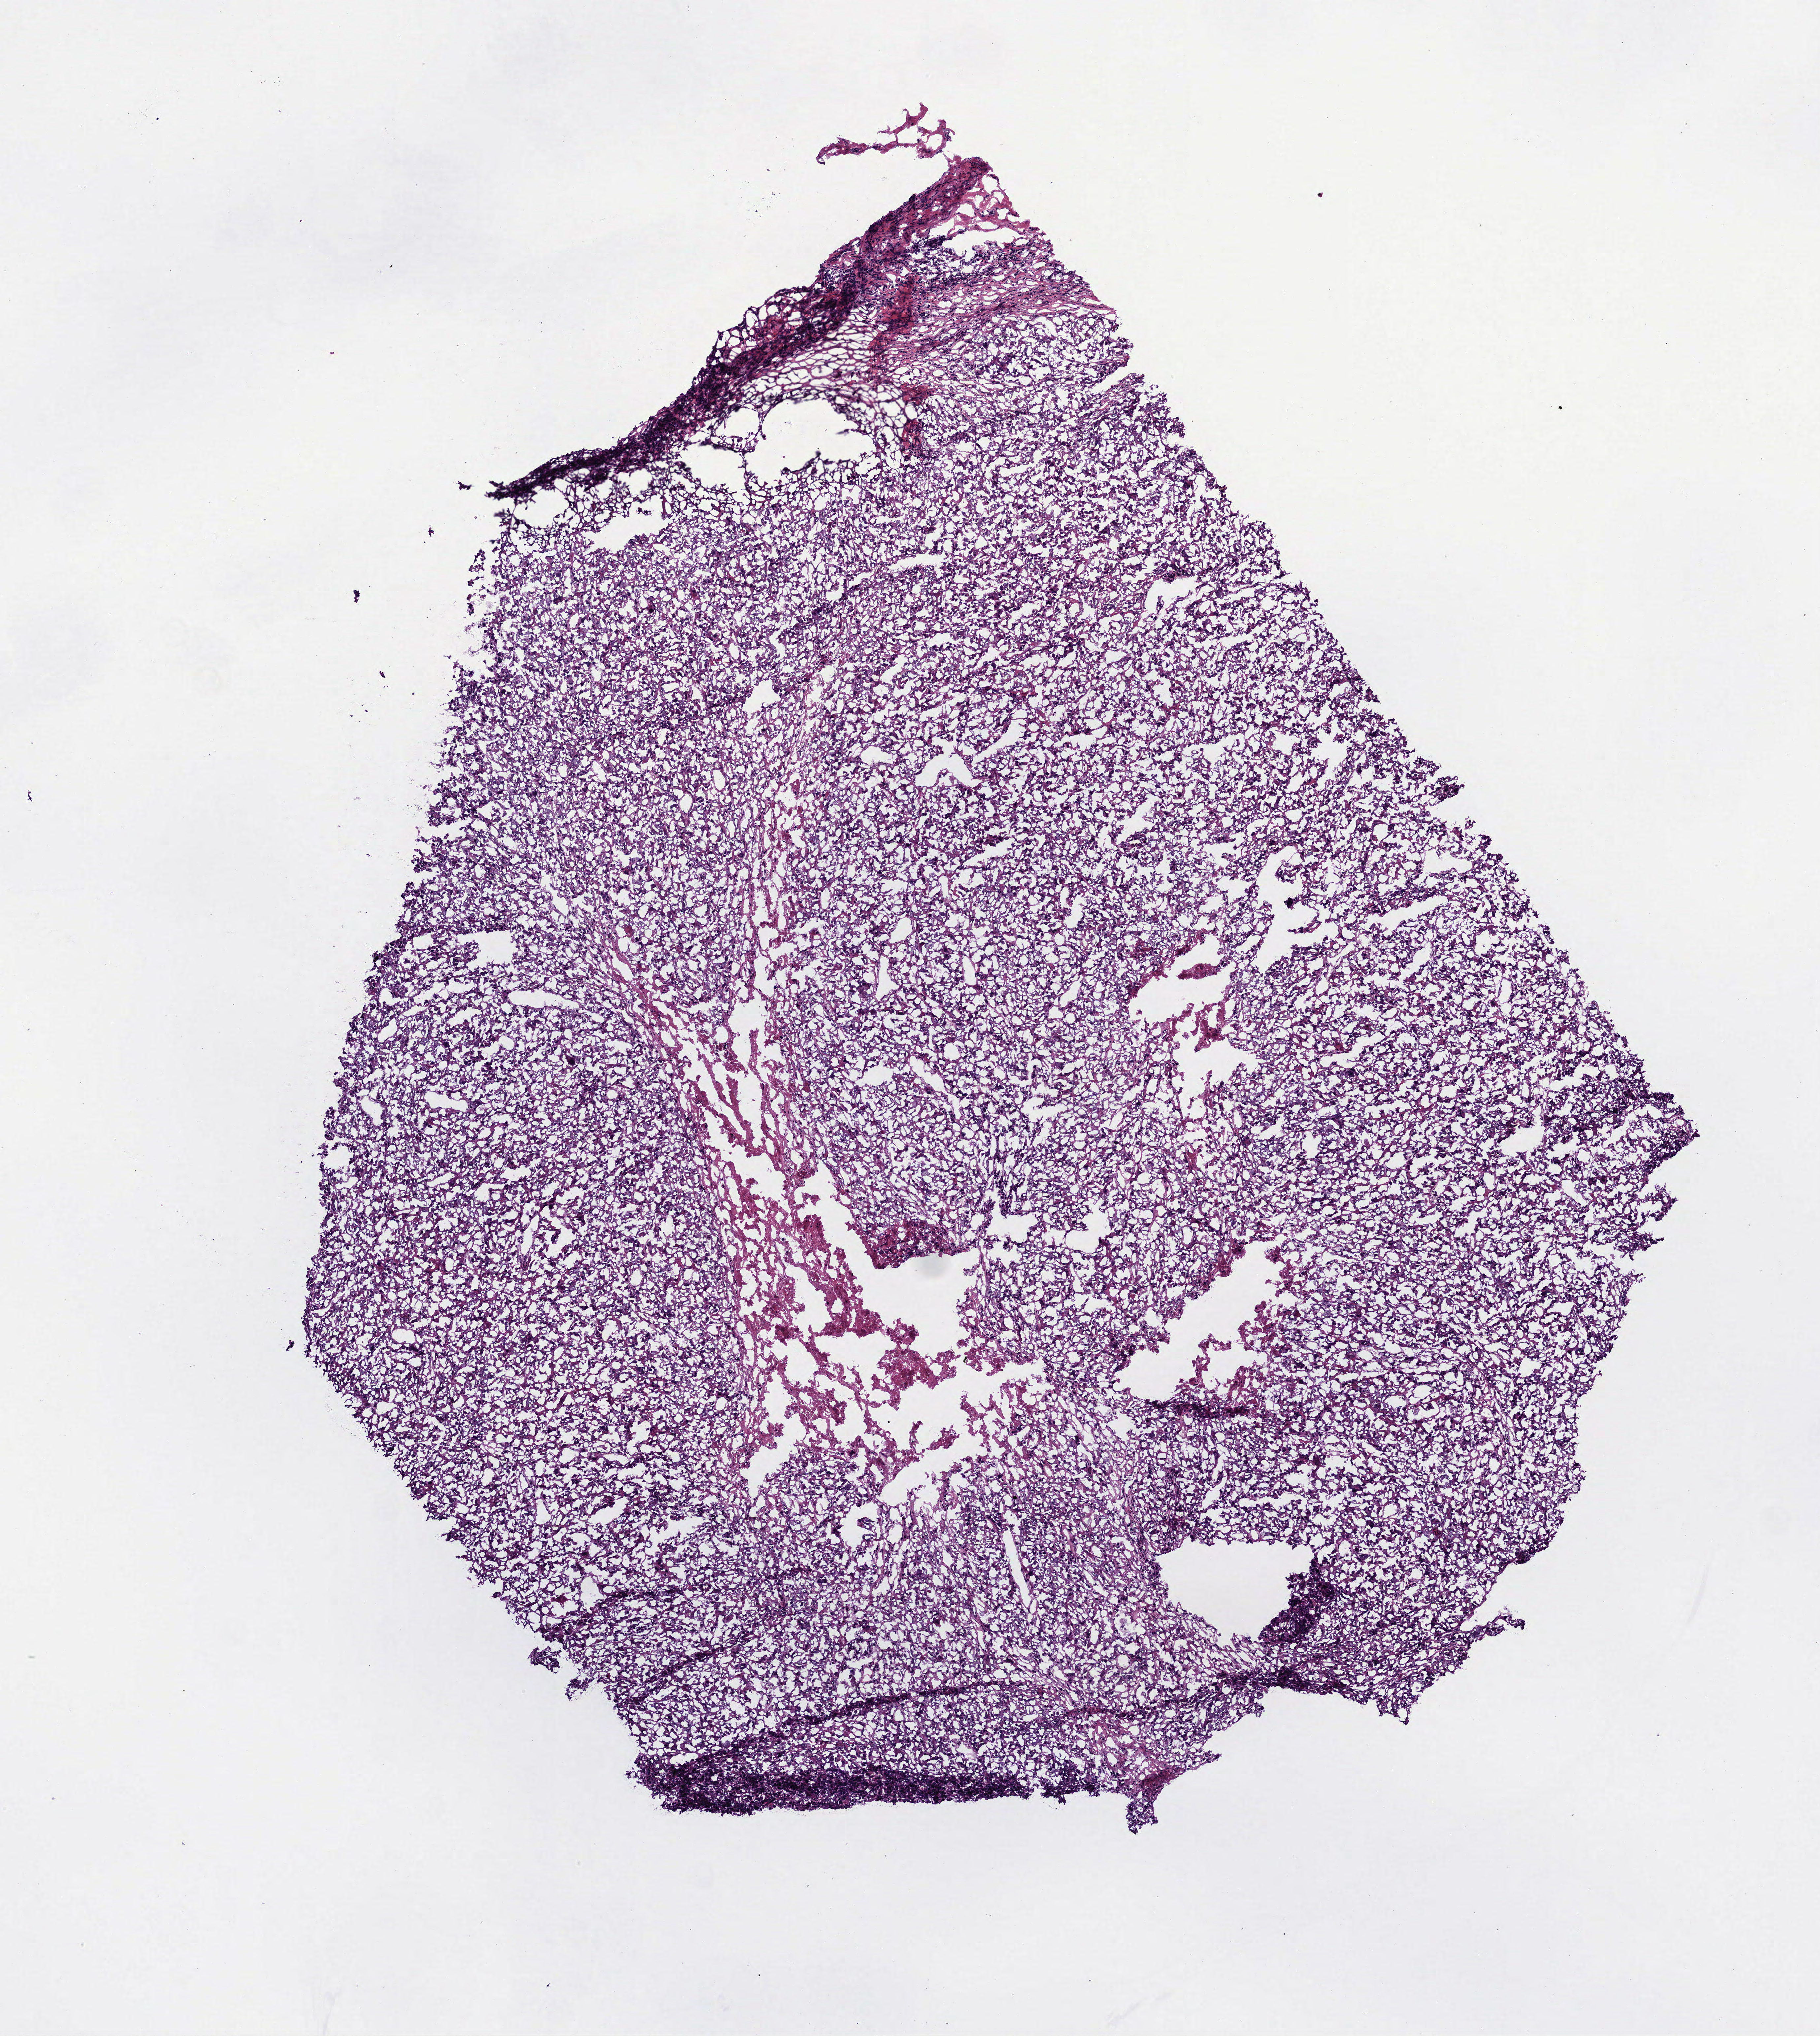
H&E whole-slide image — a low-resolution overview of the entire scanned area, about 5.6 x 6.2 mm (acquisition: 40x scan), frozen section from the bottom of the tissue portion, sample: primary tumour, lung. Patient: female, age at initial diagnosis 40 years.
Diagnosis: Adenocarcinoma, NOS (upper lobe, lung).